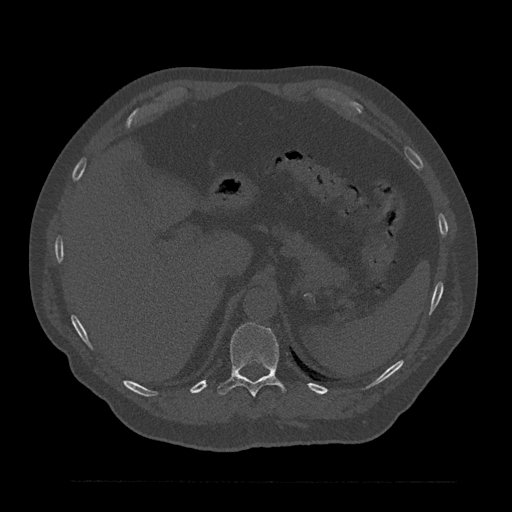
CT including the spine, one axial slice. Slice 292 of 797 in the series (ordered by position). Reconstruction kernel Br40s/3. 120 kVp. Bone window (W 1800 / L 400 HU). 0.5 mm slice thickness. 512 × 512 image matrix, field of view 430 × 430 mm. Patient: male, 61 years. From the clinical record (not read from this slice): primary cancer: prostate.
Annotated regions visible in this slice (semi-automatic segmentation, software-assisted and operator-edited):
- T11 vertebra: bounding box <217,322,286,396> (left, top, right, bottom; pixels)